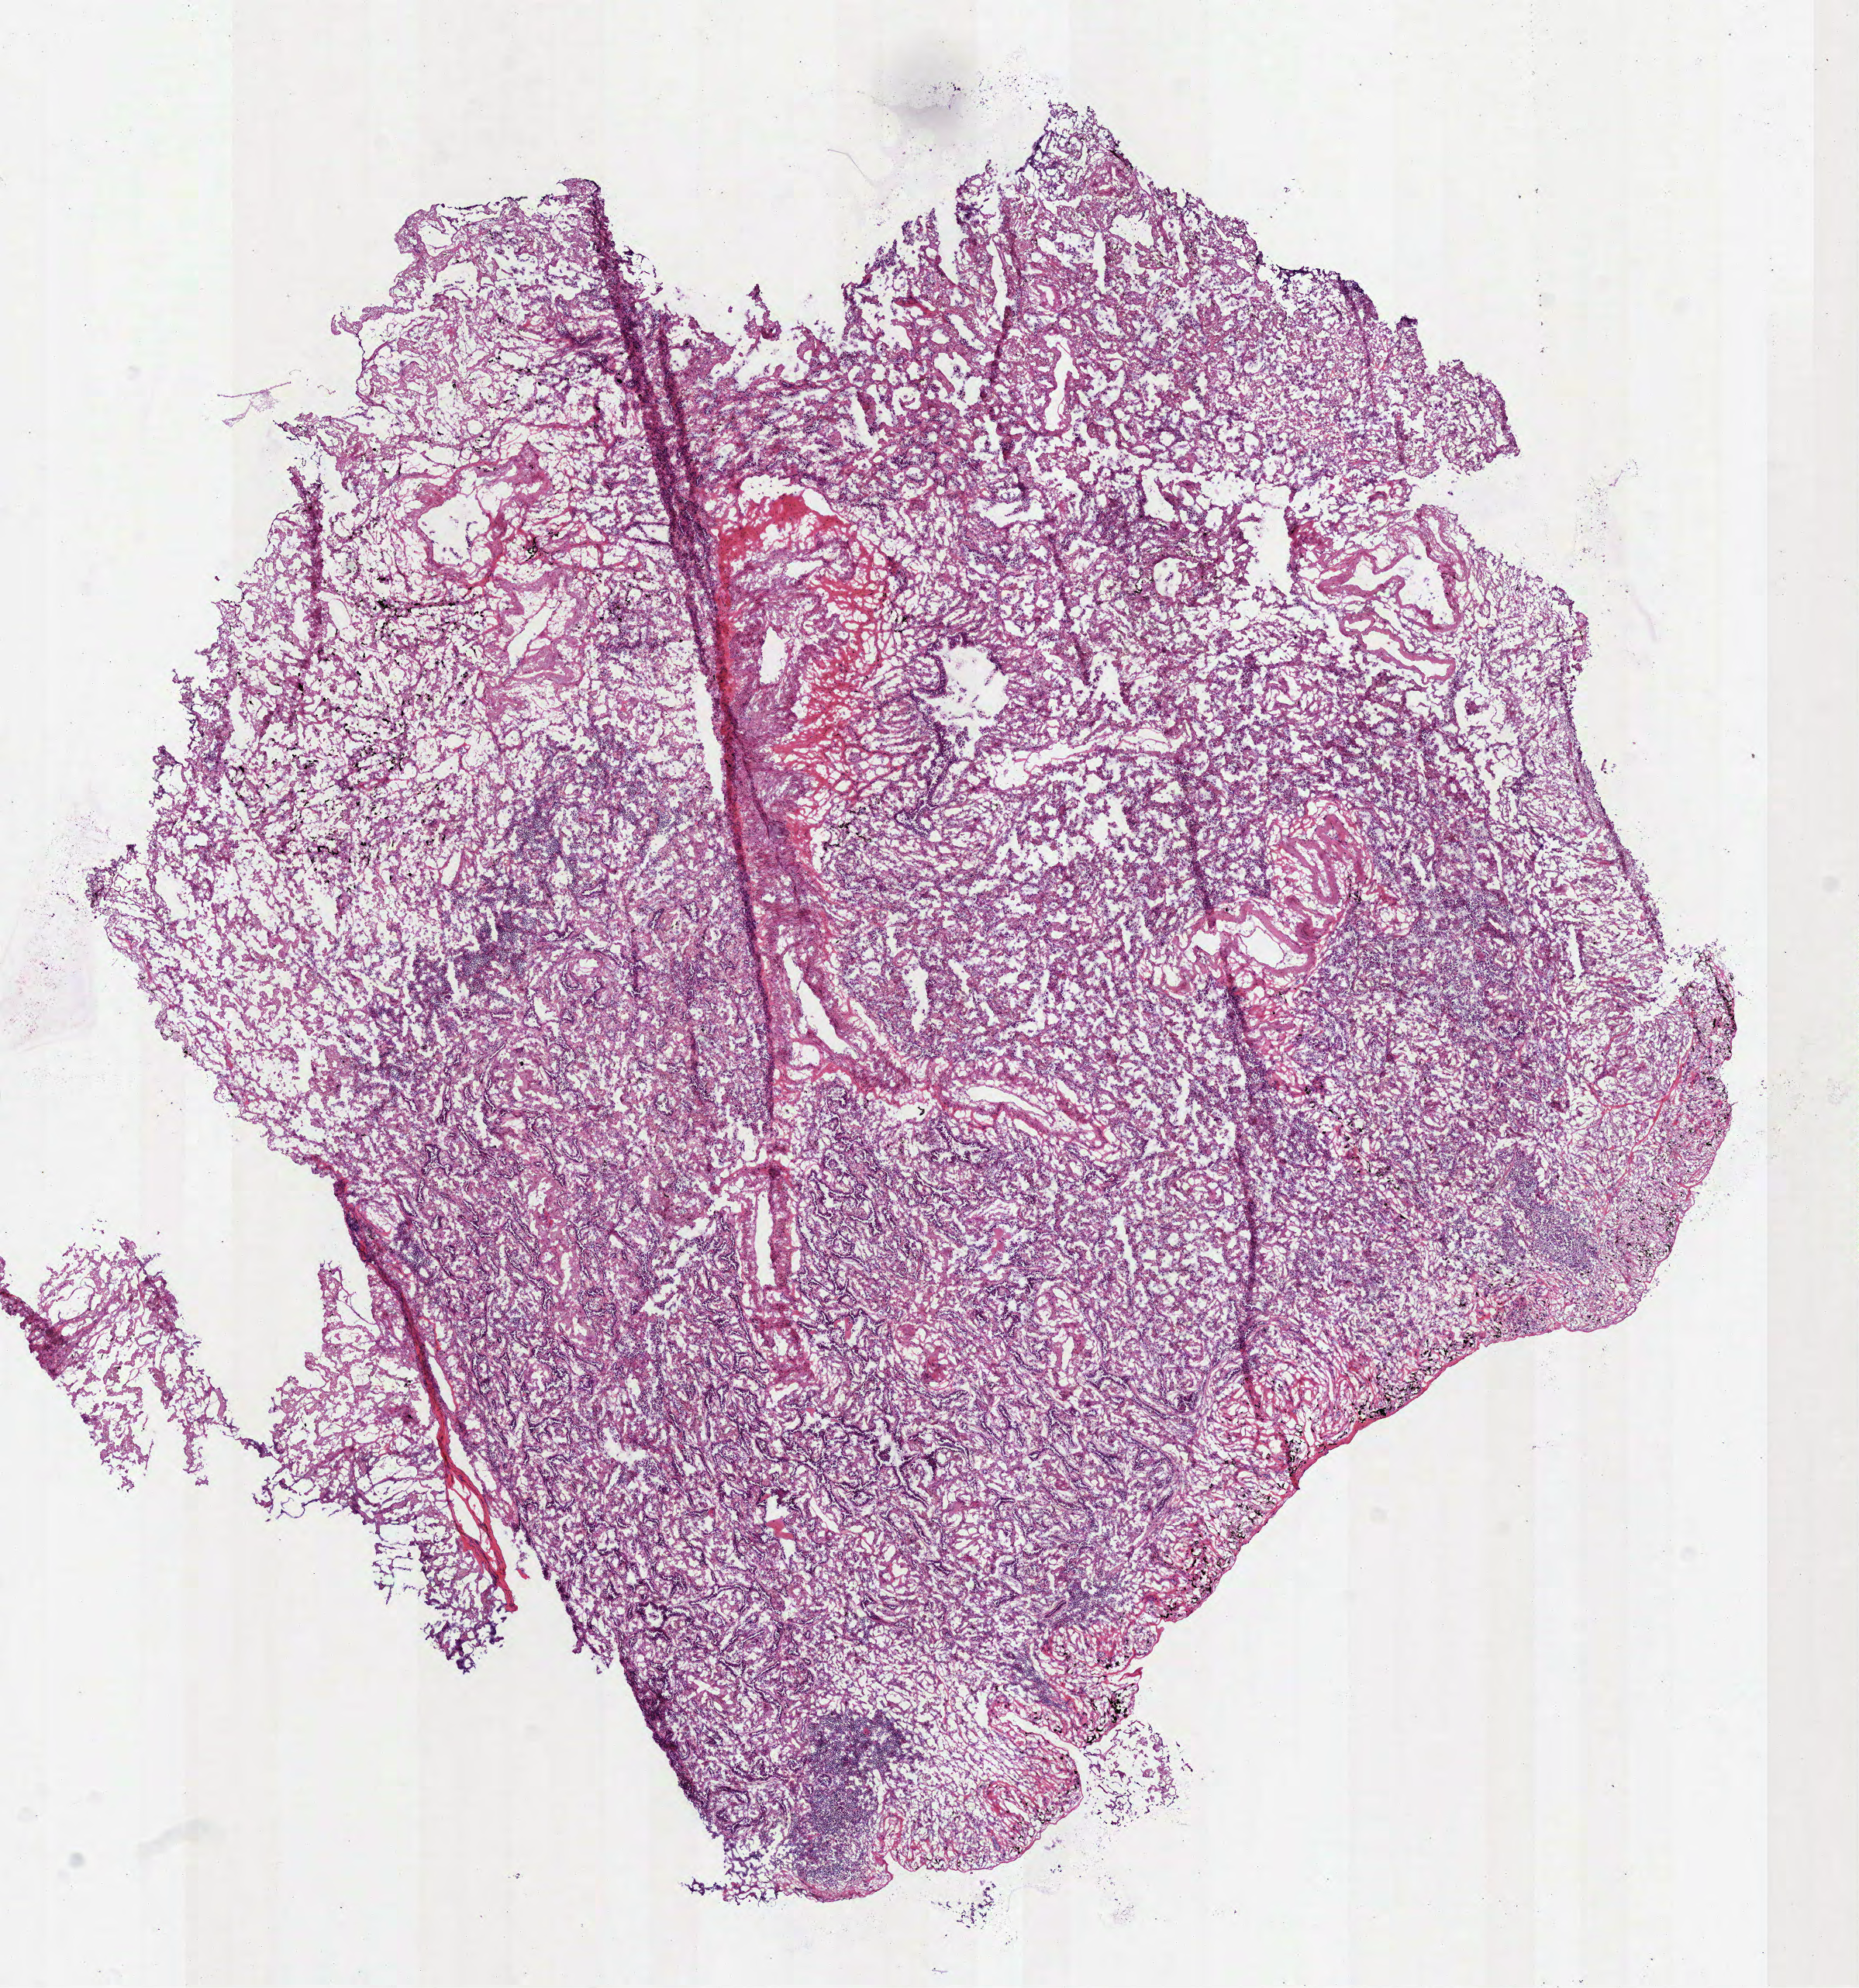
Hematoxylin and eosin (H&E) stained whole-slide image, shown as a low-resolution overview of the whole scanned area (about 9.7 x 10.3 mm); frozen section from the bottom of the tissue portion; lung, primary tumour sample. Female patient; age at initial diagnosis 63 years. Slide review estimates, as recorded: tumour cells 73%, tumour nuclei 70%, normal cells 12%, stromal cells 15%, necrosis 0%.
Histologic diagnosis: Adenocarcinoma with mixed subtypes (upper lobe, lung). Laterality: right. AJCC pathologic stage: IA.